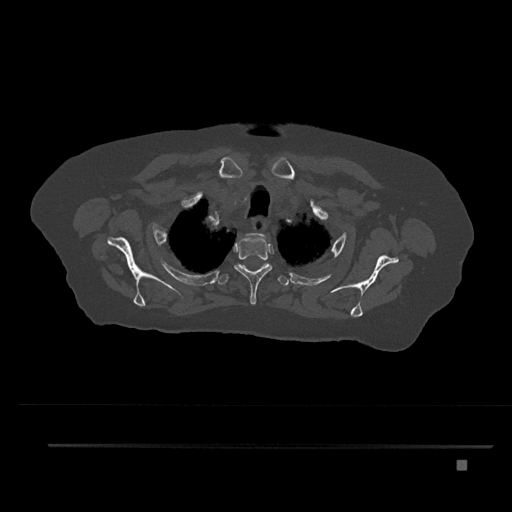
CT including the spine, one axial slice; position 664 of 797 along the scan axis; reconstruction kernel Br40s/3; 120 kVp; bone window (W 1800 / L 400 HU); 0.5 mm slice thickness; 512 × 512 image matrix, field of view 437 × 437 mm. Patient: female, 76 years. From the clinical record (not read from this slice): primary cancer: lung; vertebrae with lytic lesions (as recorded): T11, L3.
Annotated regions visible in this slice (semi-automatically segmented with operator editing):
- T1 vertebra: bounding box [x1, y1, x2, y2] px = [246, 233, 267, 242]
- T2 vertebra: [234, 237, 272, 305]
- T3 vertebra: [219, 262, 289, 286]